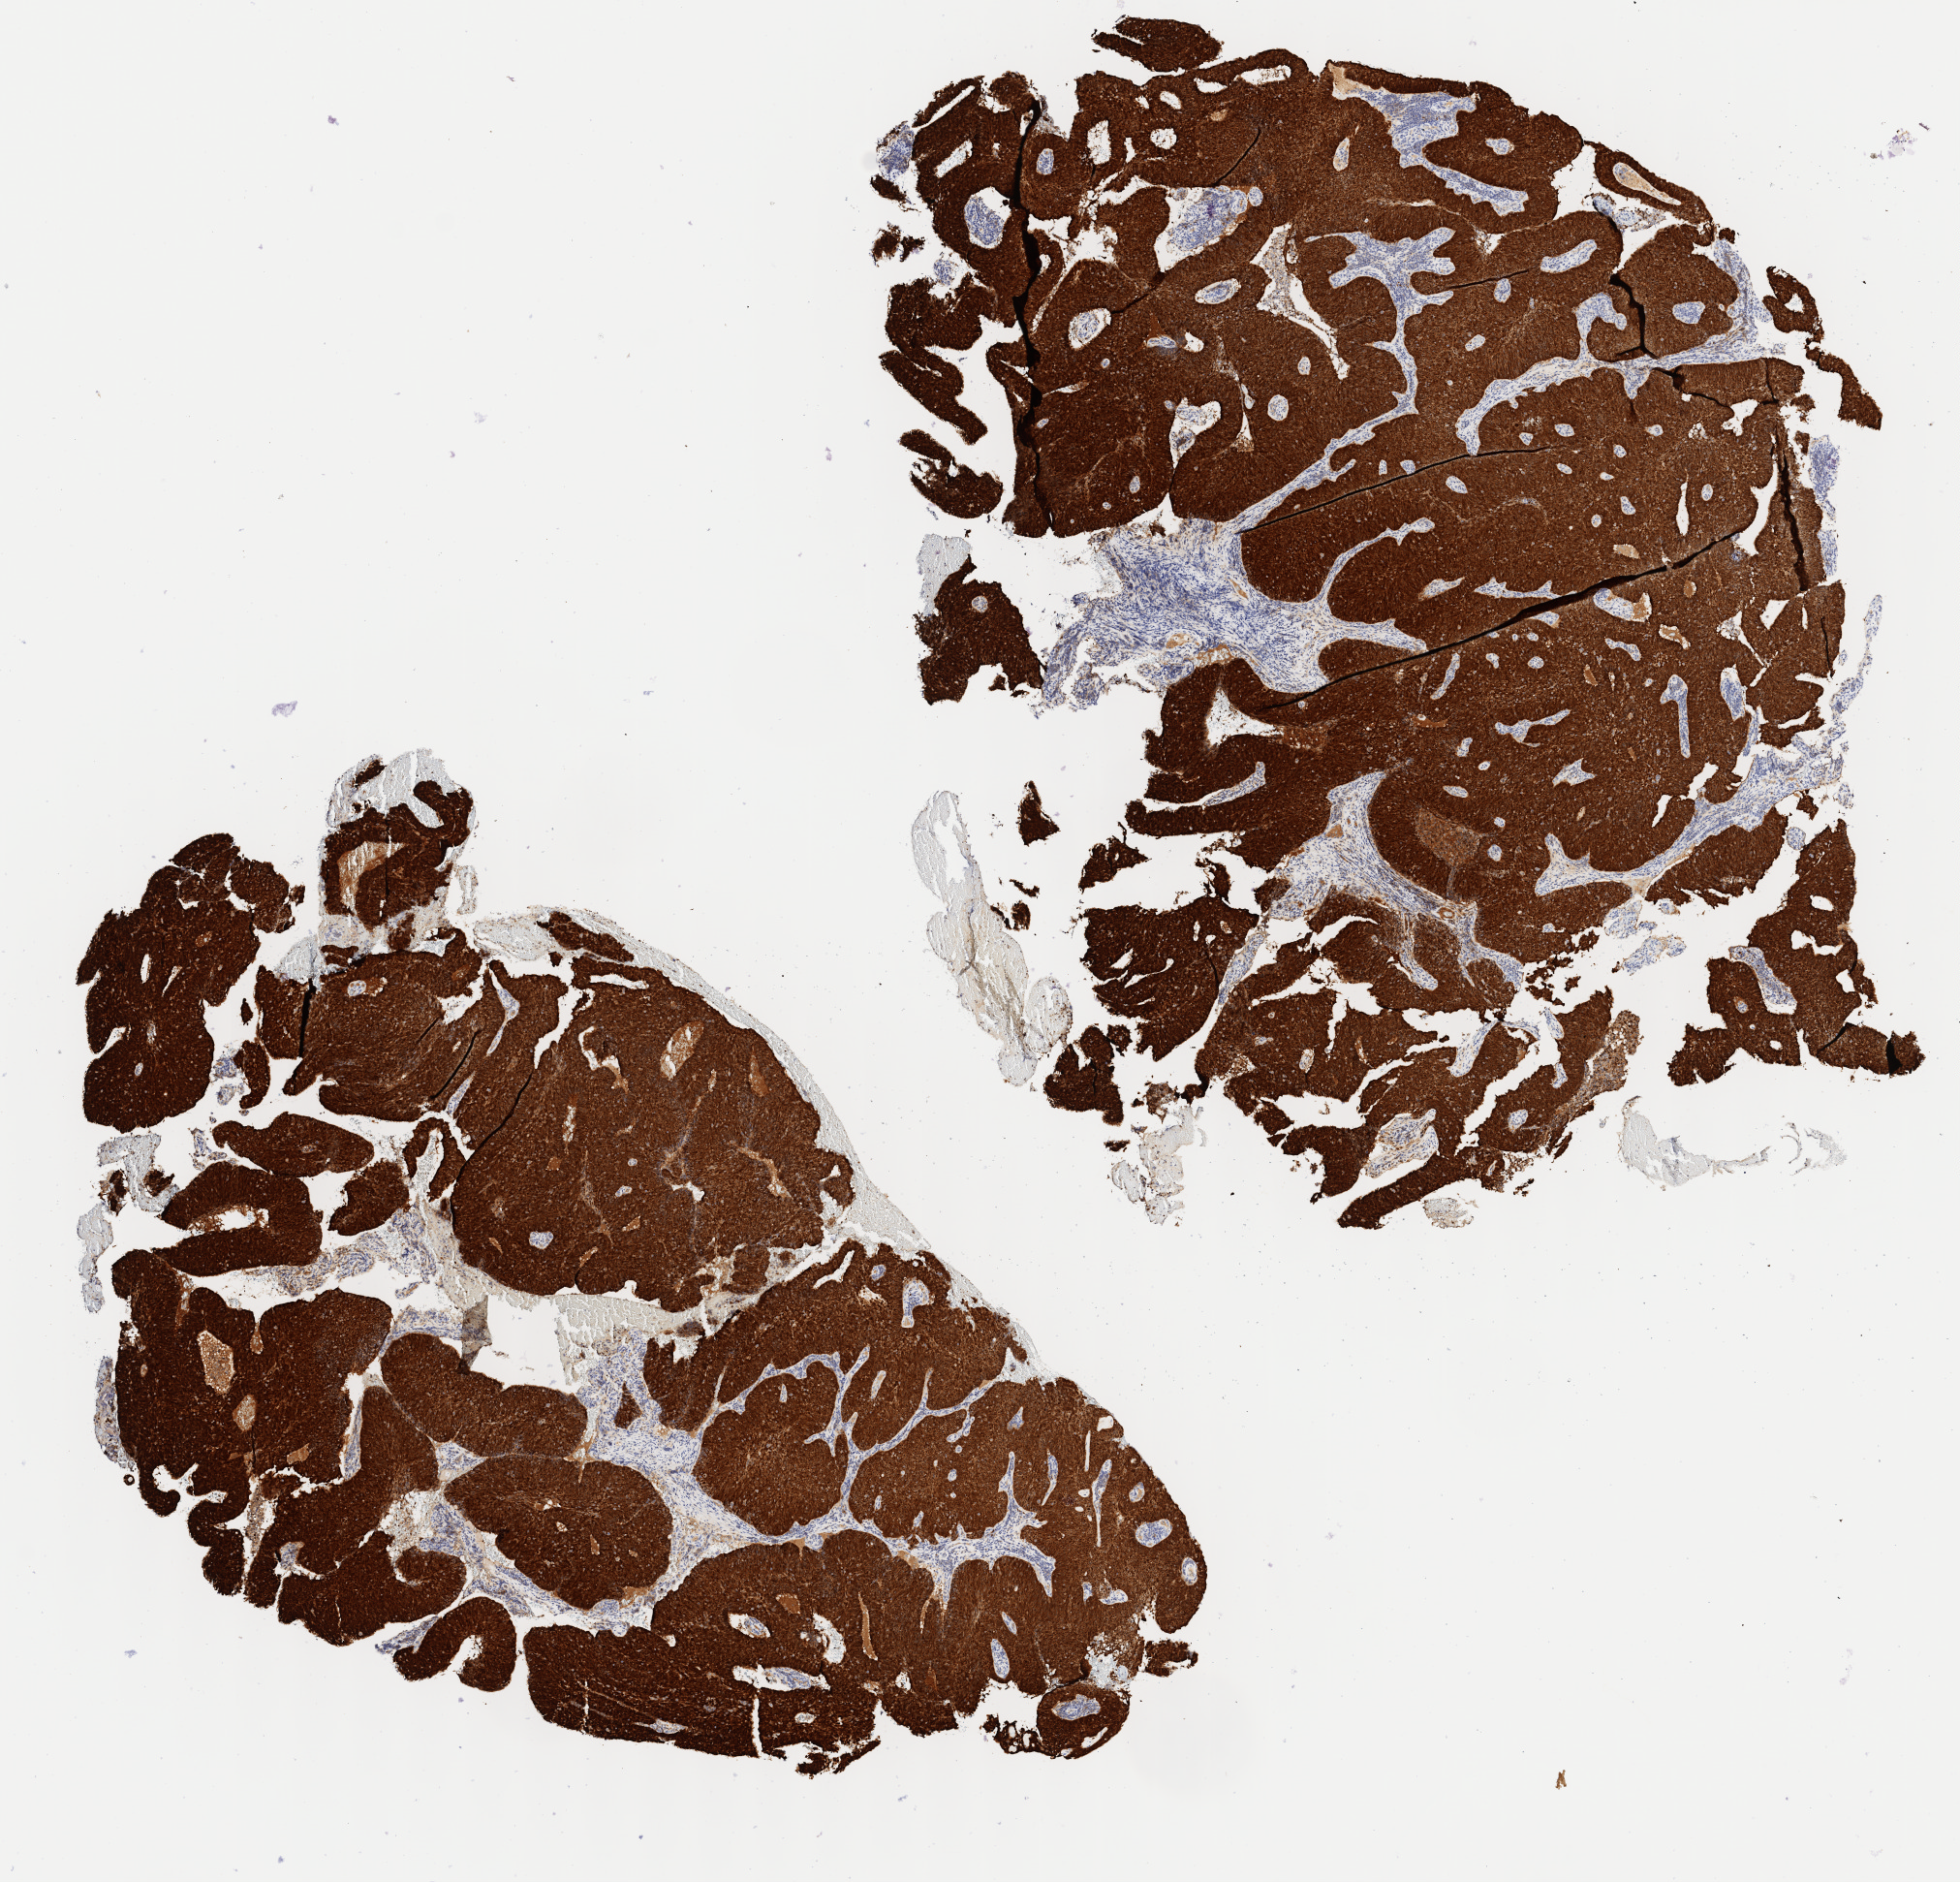
IHC for p16 (p16INK4a), whole-slide image, shown as a low-resolution overview of the whole scanned area (about 8.0 x 7.7 mm); specimen: tumor tissue; site: cervix. Female patient, age 78 years.
* histologic diagnosis: Squamous cell carcinoma, large cell, nonkeratinizing, NOS